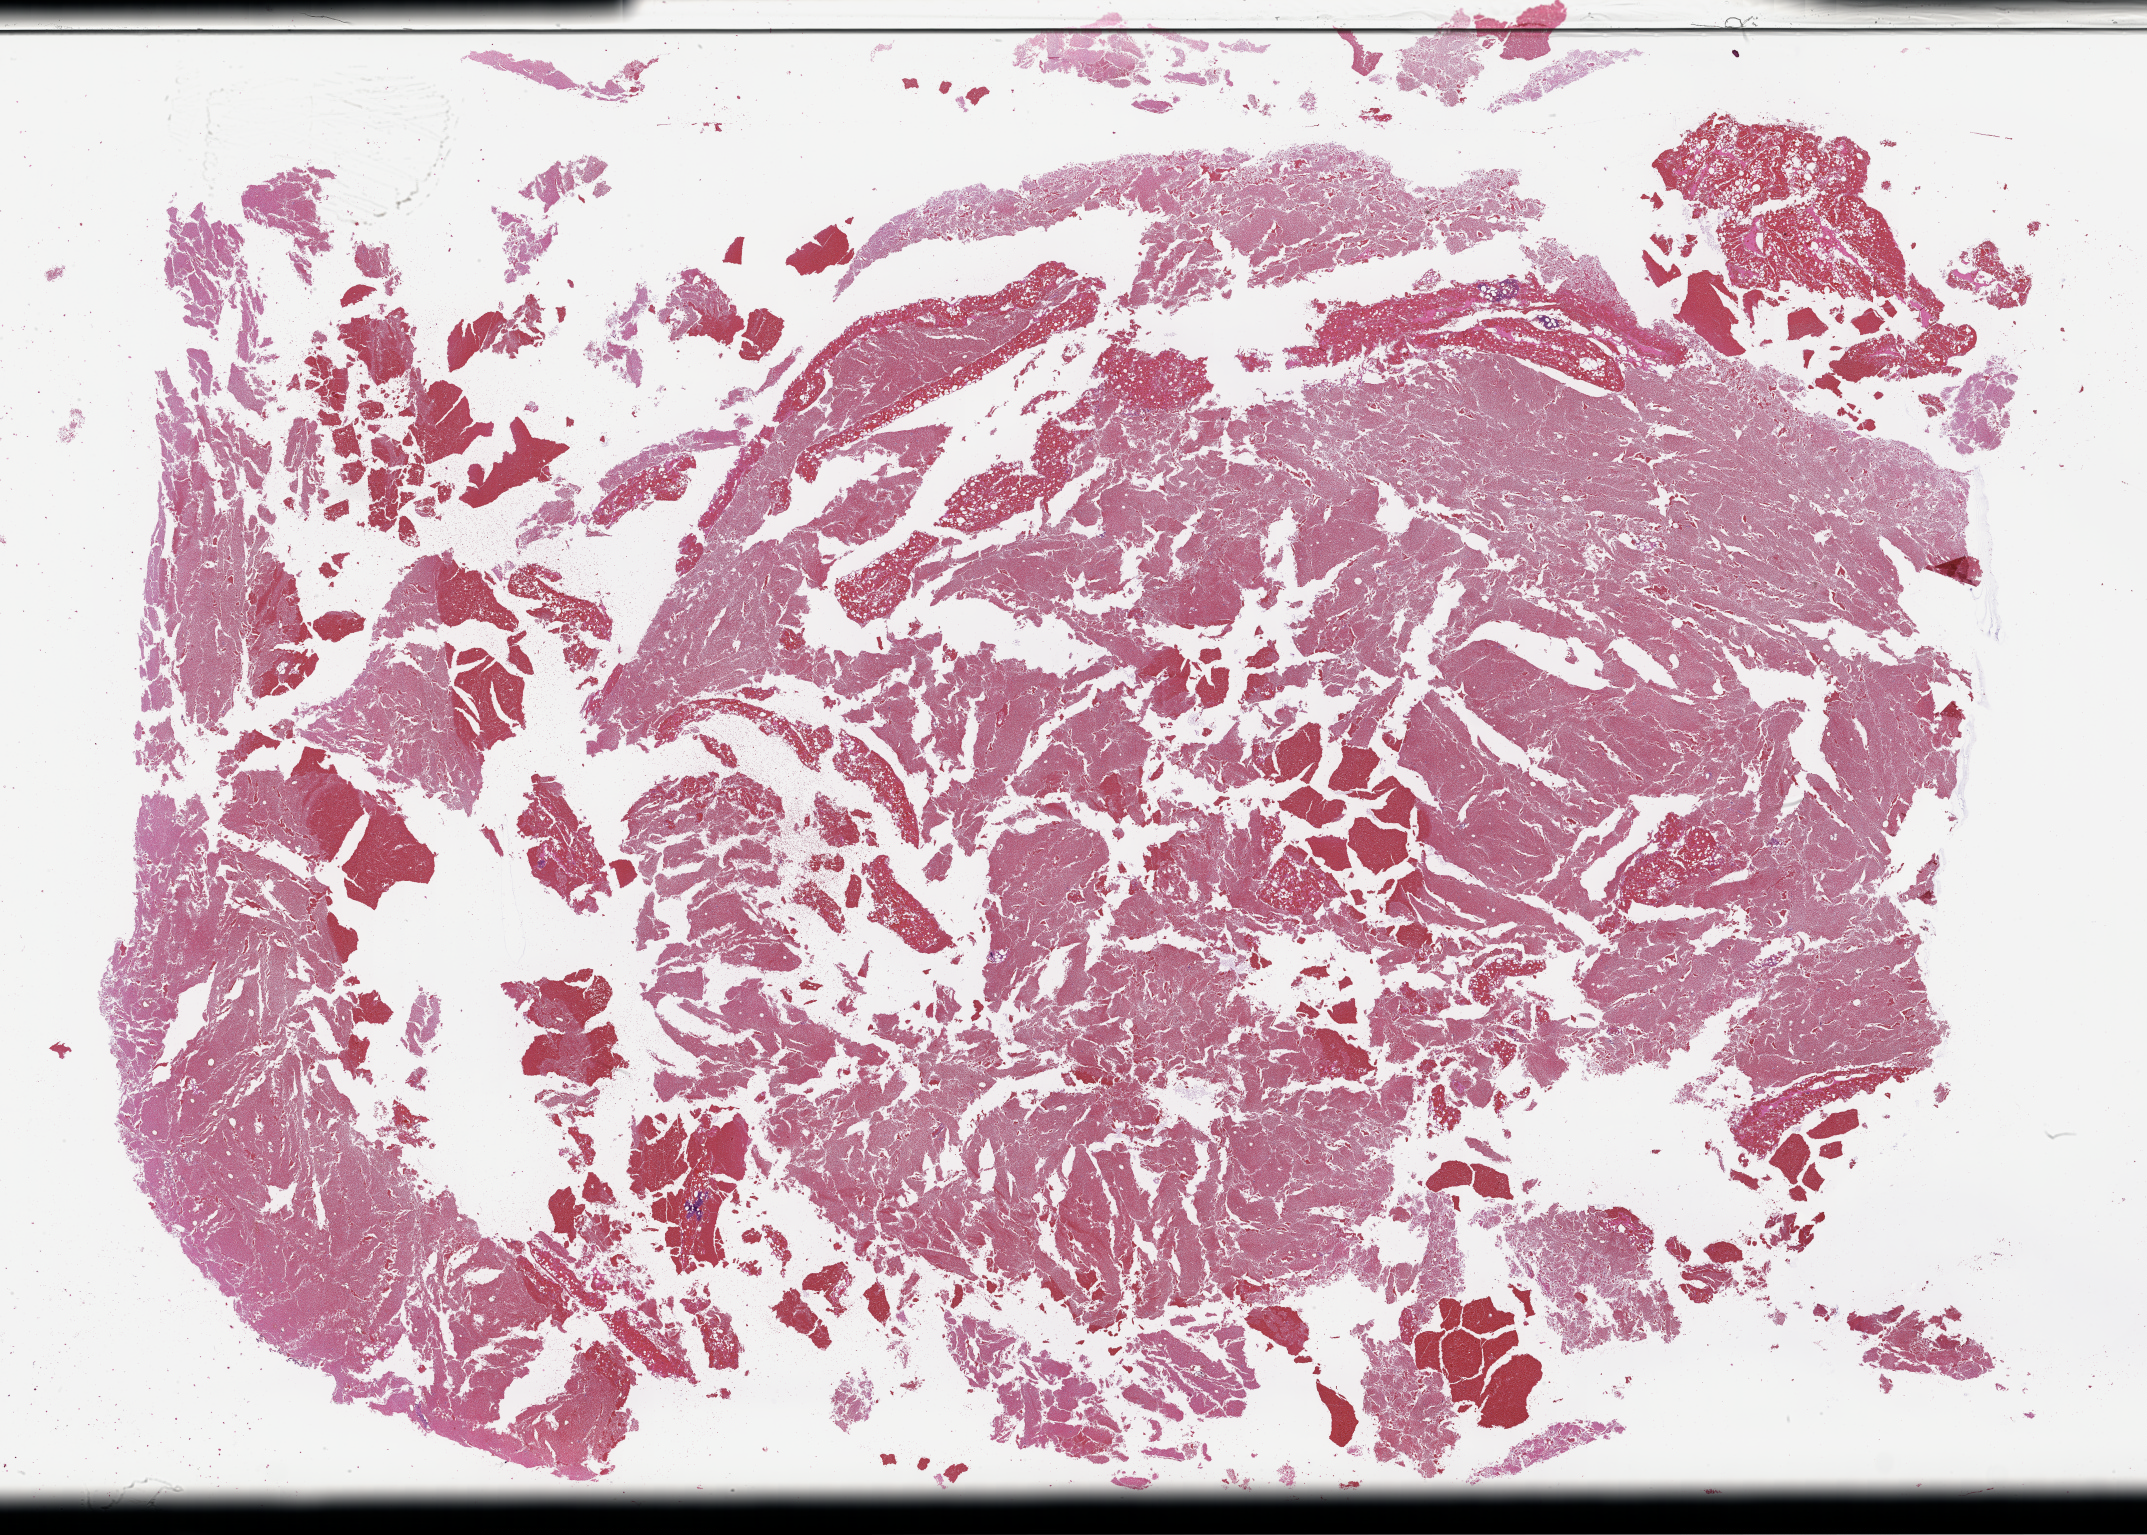
Hematoxylin and eosin (H&E) whole-slide image — a low-resolution overview of the entire scanned area, about 34.7 x 24.8 mm; formalin-fixed paraffin-embedded section; tissue site: bone marrow; archival tissue. Male patient.
• this section: primary tumour tissue
• diagnosis: Plasma Cell Myeloma